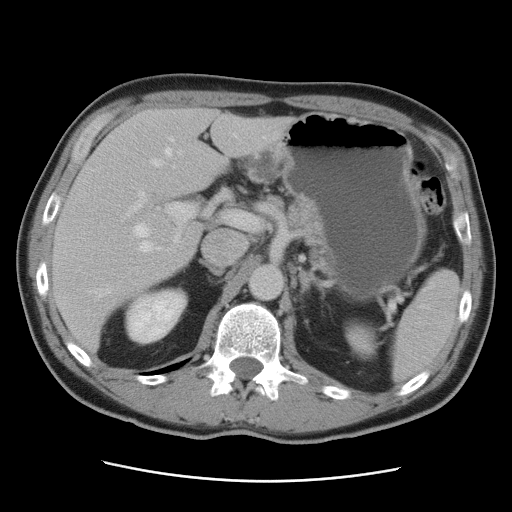
Contrast-enhanced abdominal CT, one axial slice; slice 55 of 89 in the series (ordered by position); 120 kVp; intravenous contrast given; soft-tissue window (W 400 / L 40 HU); 5 mm slice thickness; 512 × 512 image matrix. Male patient, age 59 years. From the clinical record (not read from this slice): diagnosis: colorectal cancer liver metastases, imaged before liver resection; multiple liver metastases: yes; largest metastasis: 0.6 cm; disease in both lobes: yes.
Outlined on this slice (expert manual segmentation):
- hepatic veins: bounding box <88,134,265,298> (left, top, right, bottom; pixels)
- liver: <53,108,292,354>
- planned liver remnant (the part of the liver to remain after resection): <73,108,229,238>
- portal vein (with intrahepatic branches): <127,191,257,271>